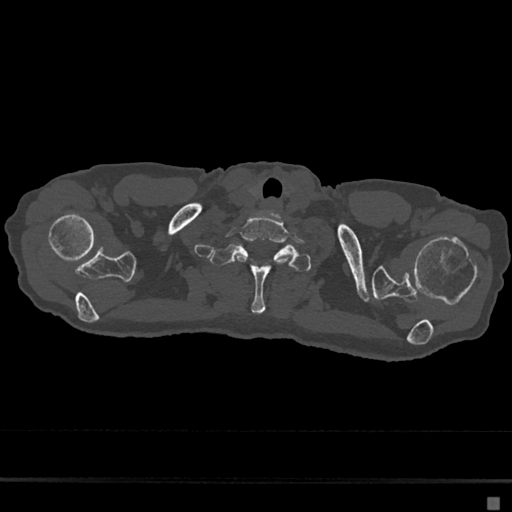
CT including the spine, one axial slice. Slice 624 of 797 in the series (ordered by position). 120 kVp. Bone window (W 1800 / L 400 HU). 0.5 mm slice thickness. 512 × 512 image matrix, field of view 360 × 360 mm. Patient: female, 68 years. Case-level facts recorded for this patient, not image findings: primary cancer: renal.
Outlined on this slice (semi-automatic segmentation, software-assisted and operator-edited):
- T1 vertebra: bounding box <210,244,312,314> (left, top, right, bottom; pixels)